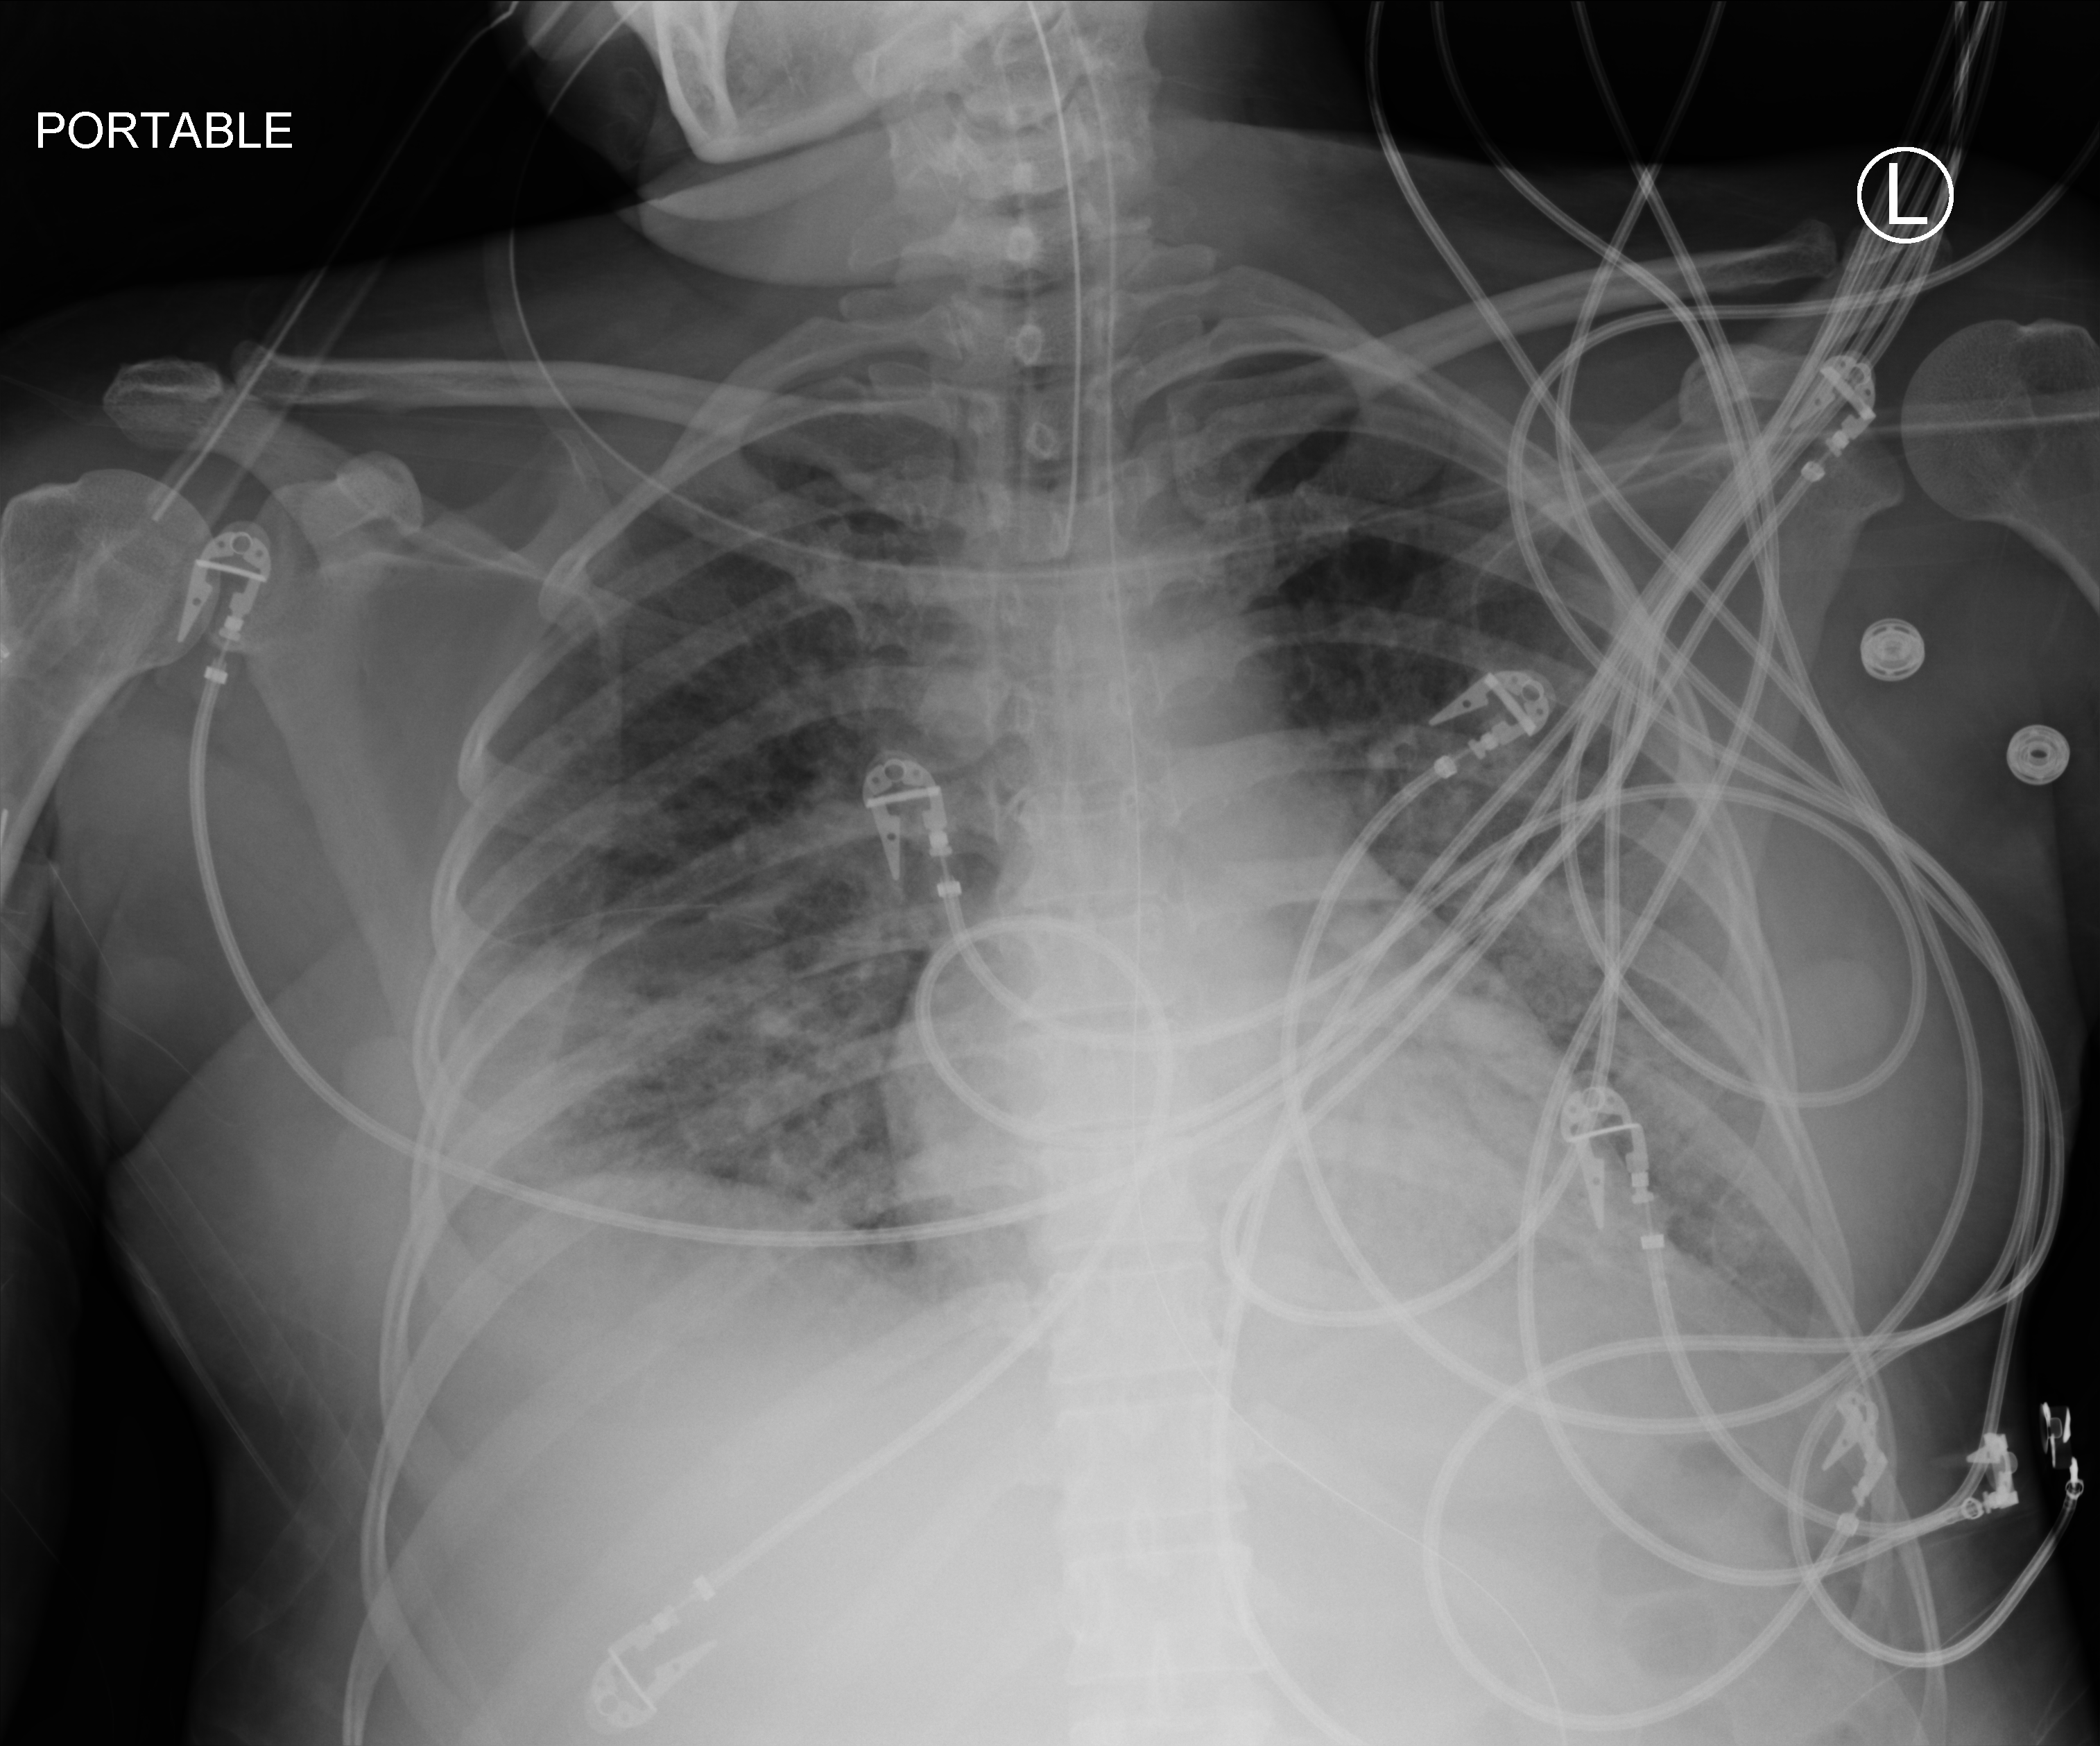
Portable chest radiograph, anteroposterior (AP) projection. Patient hospitalised with COVID-19; female, aged 18–59 years.
Admission-level facts for this patient (not findings on this image; timing relative to this image not recorded): mechanically ventilated during this hospital stay: yes; admitted to intensive care during this hospital stay: yes.